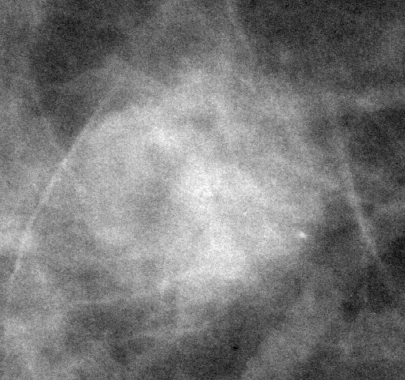
Crop from a digitized film mammogram around one marked abnormality; right breast; CC view; BI-RADS breast density category 1 (scale 1–4).
Marked abnormality: mass, shape round, margins microlobulated; BI-RADS assessment category 4; pathology (as recorded): malignant.